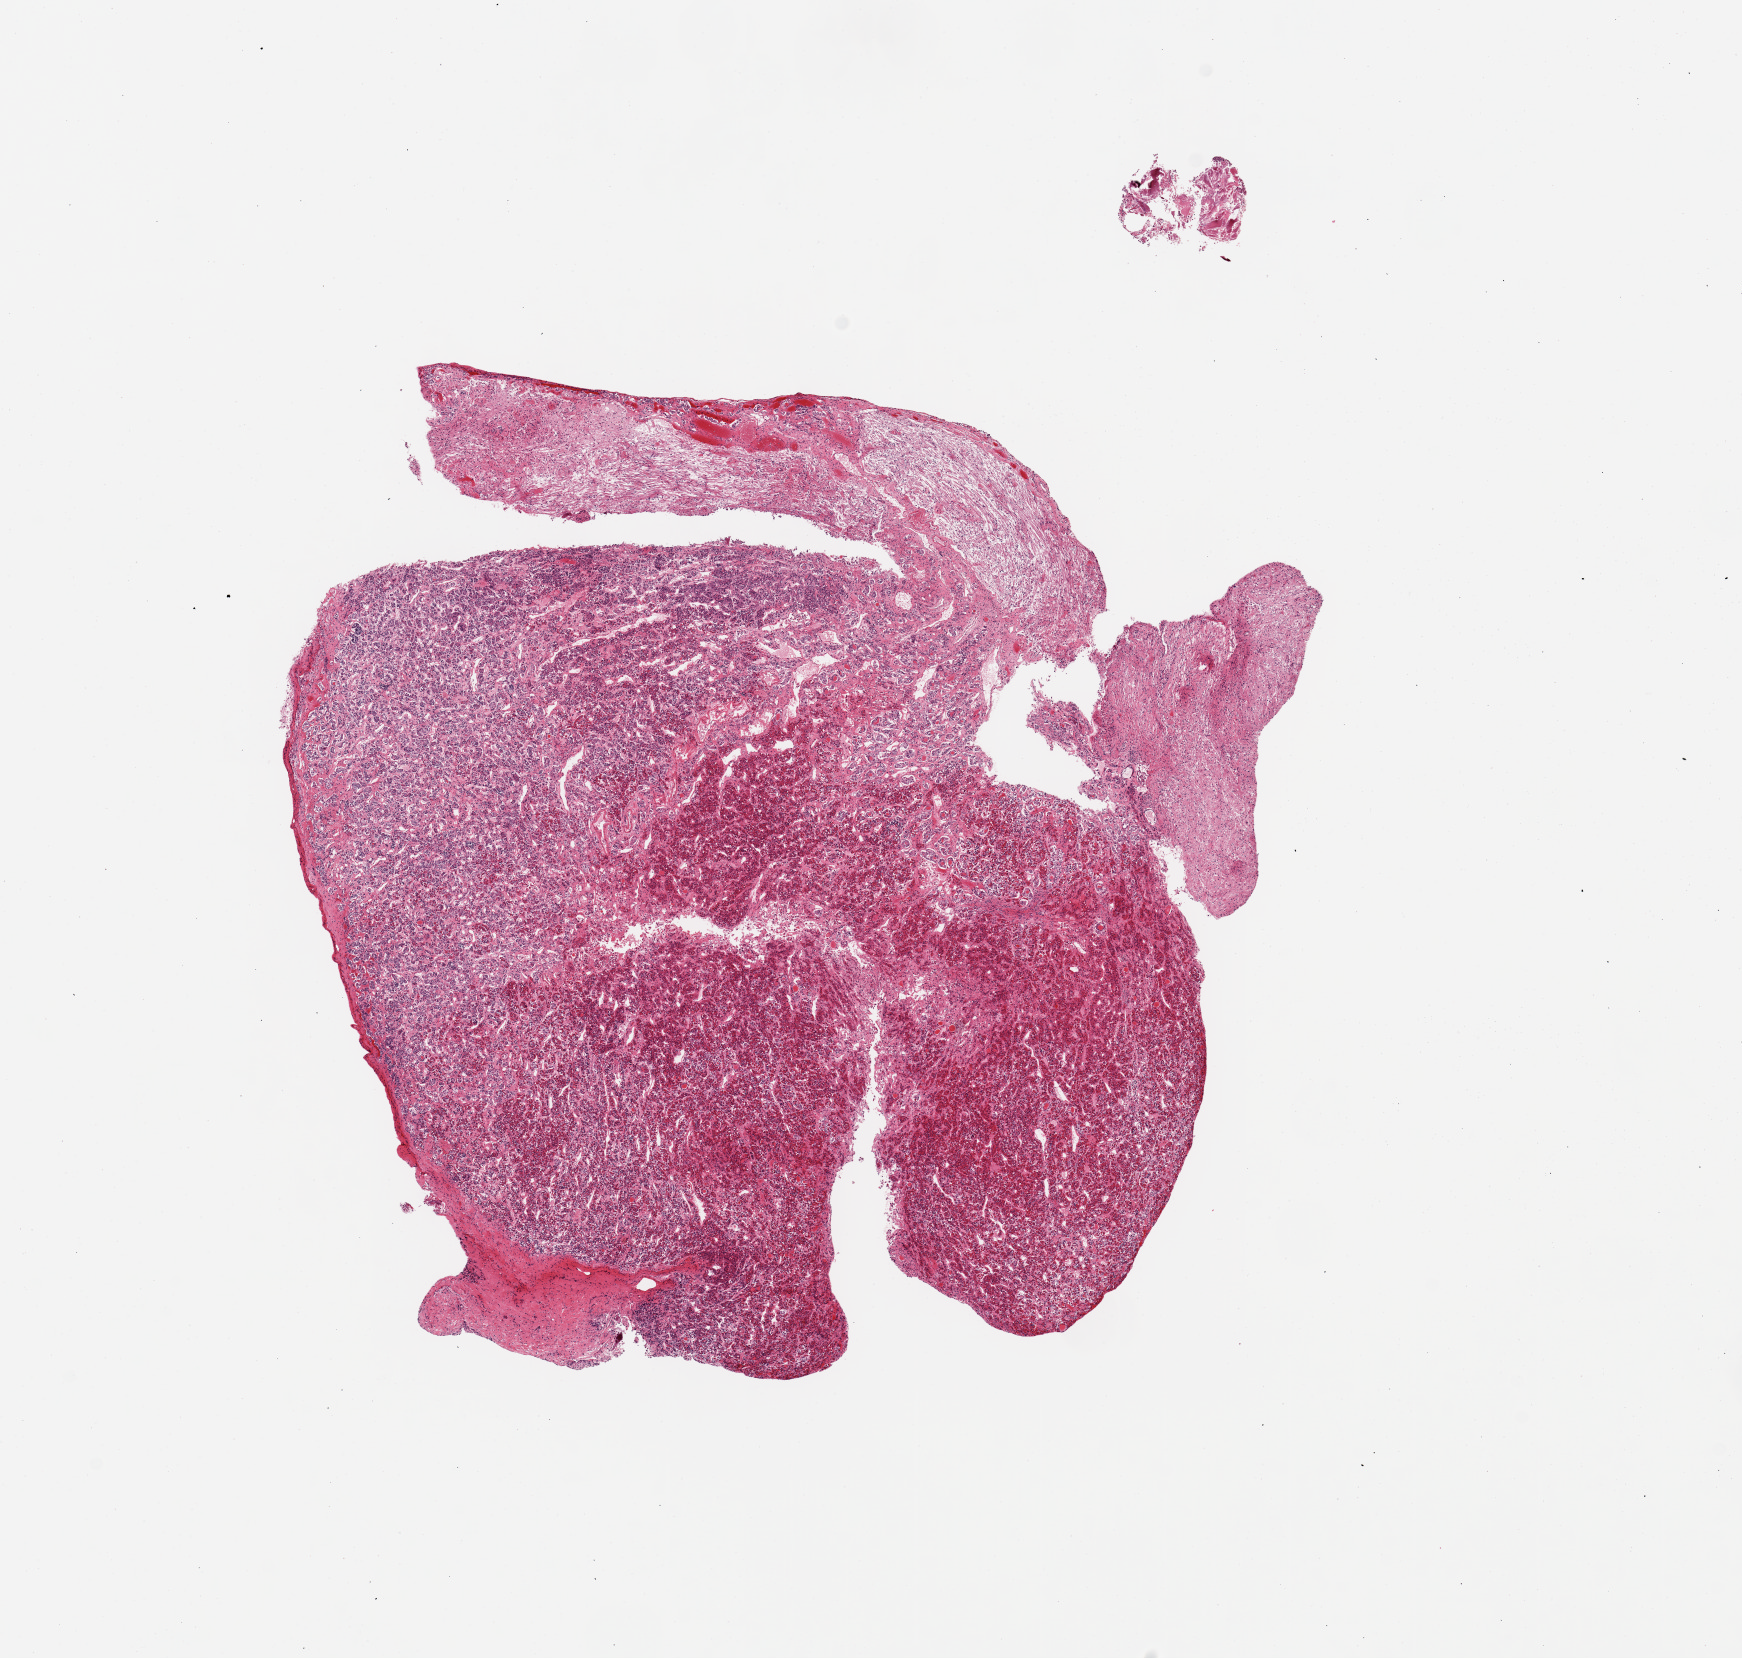
Whole-slide image, haematoxylin and eosin stain, brightfield, shown as a low-resolution overview of the whole scanned area (about 13.8 x 13.1 mm, slide scanned at 20x), PAXgene-fixed, paraffin-embedded tissue, sampled site (target tissue): pituitary, tissue donor sample.
• review note (as recorded): 1 piece; mostly adenohypophysis; neurohypophysis